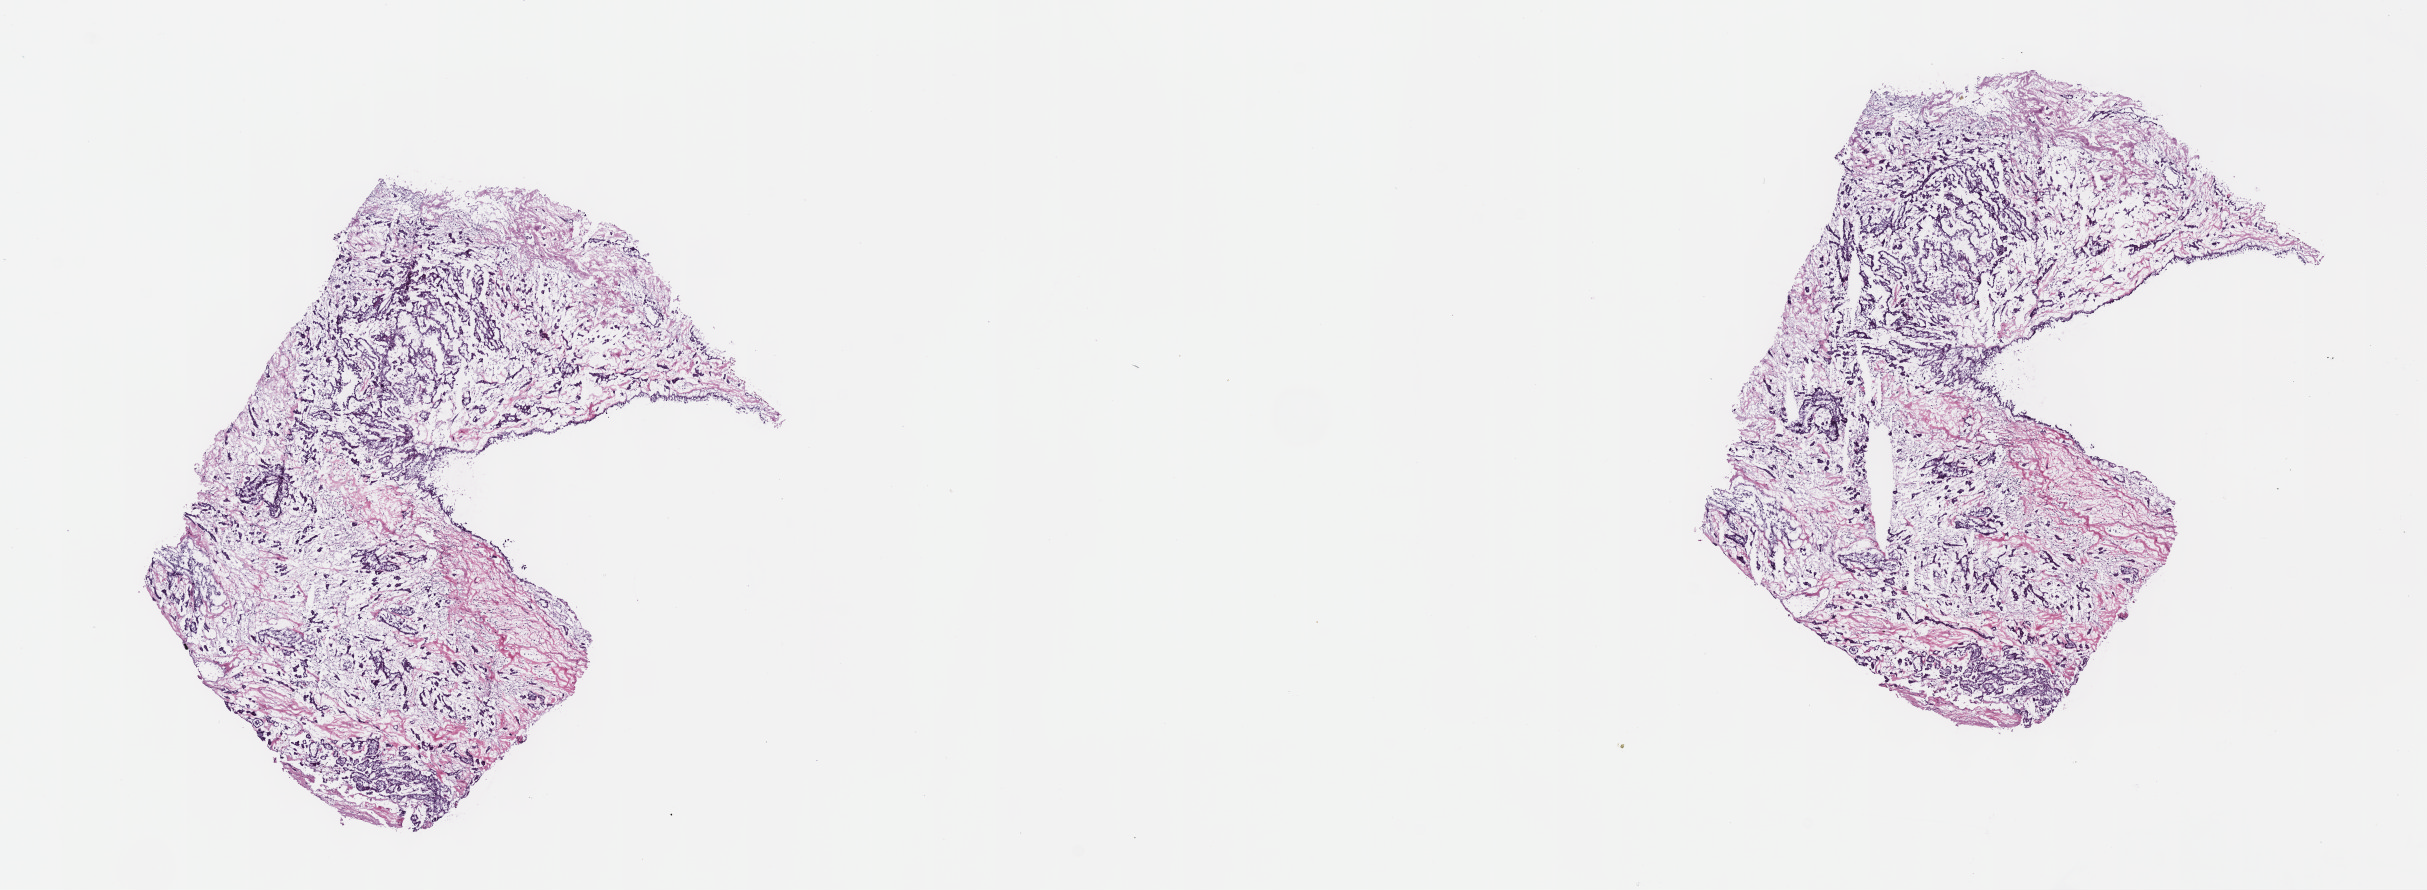
Whole-slide histology image, H&E-stained — shown as a low-resolution overview of the whole scanned area (about 19.6 x 7.2 mm, acquisition: 40x scan), frozen section, sample: primary tumour, kidney. Female patient; age at initial diagnosis 52 years. Composition of this section per pathologist review: tumour cells 100%, tumour nuclei 65%, normal cells 0%, stromal cells 0%, necrosis 0%. Infiltration values recorded for this section: lymphocyte infiltration 5%, monocyte infiltration 4%, neutrophil infiltration 0%.
- histologic diagnosis: Papillary adenocarcinoma, NOS
- laterality: right
- AJCC pathologic stage: II (7th edition)